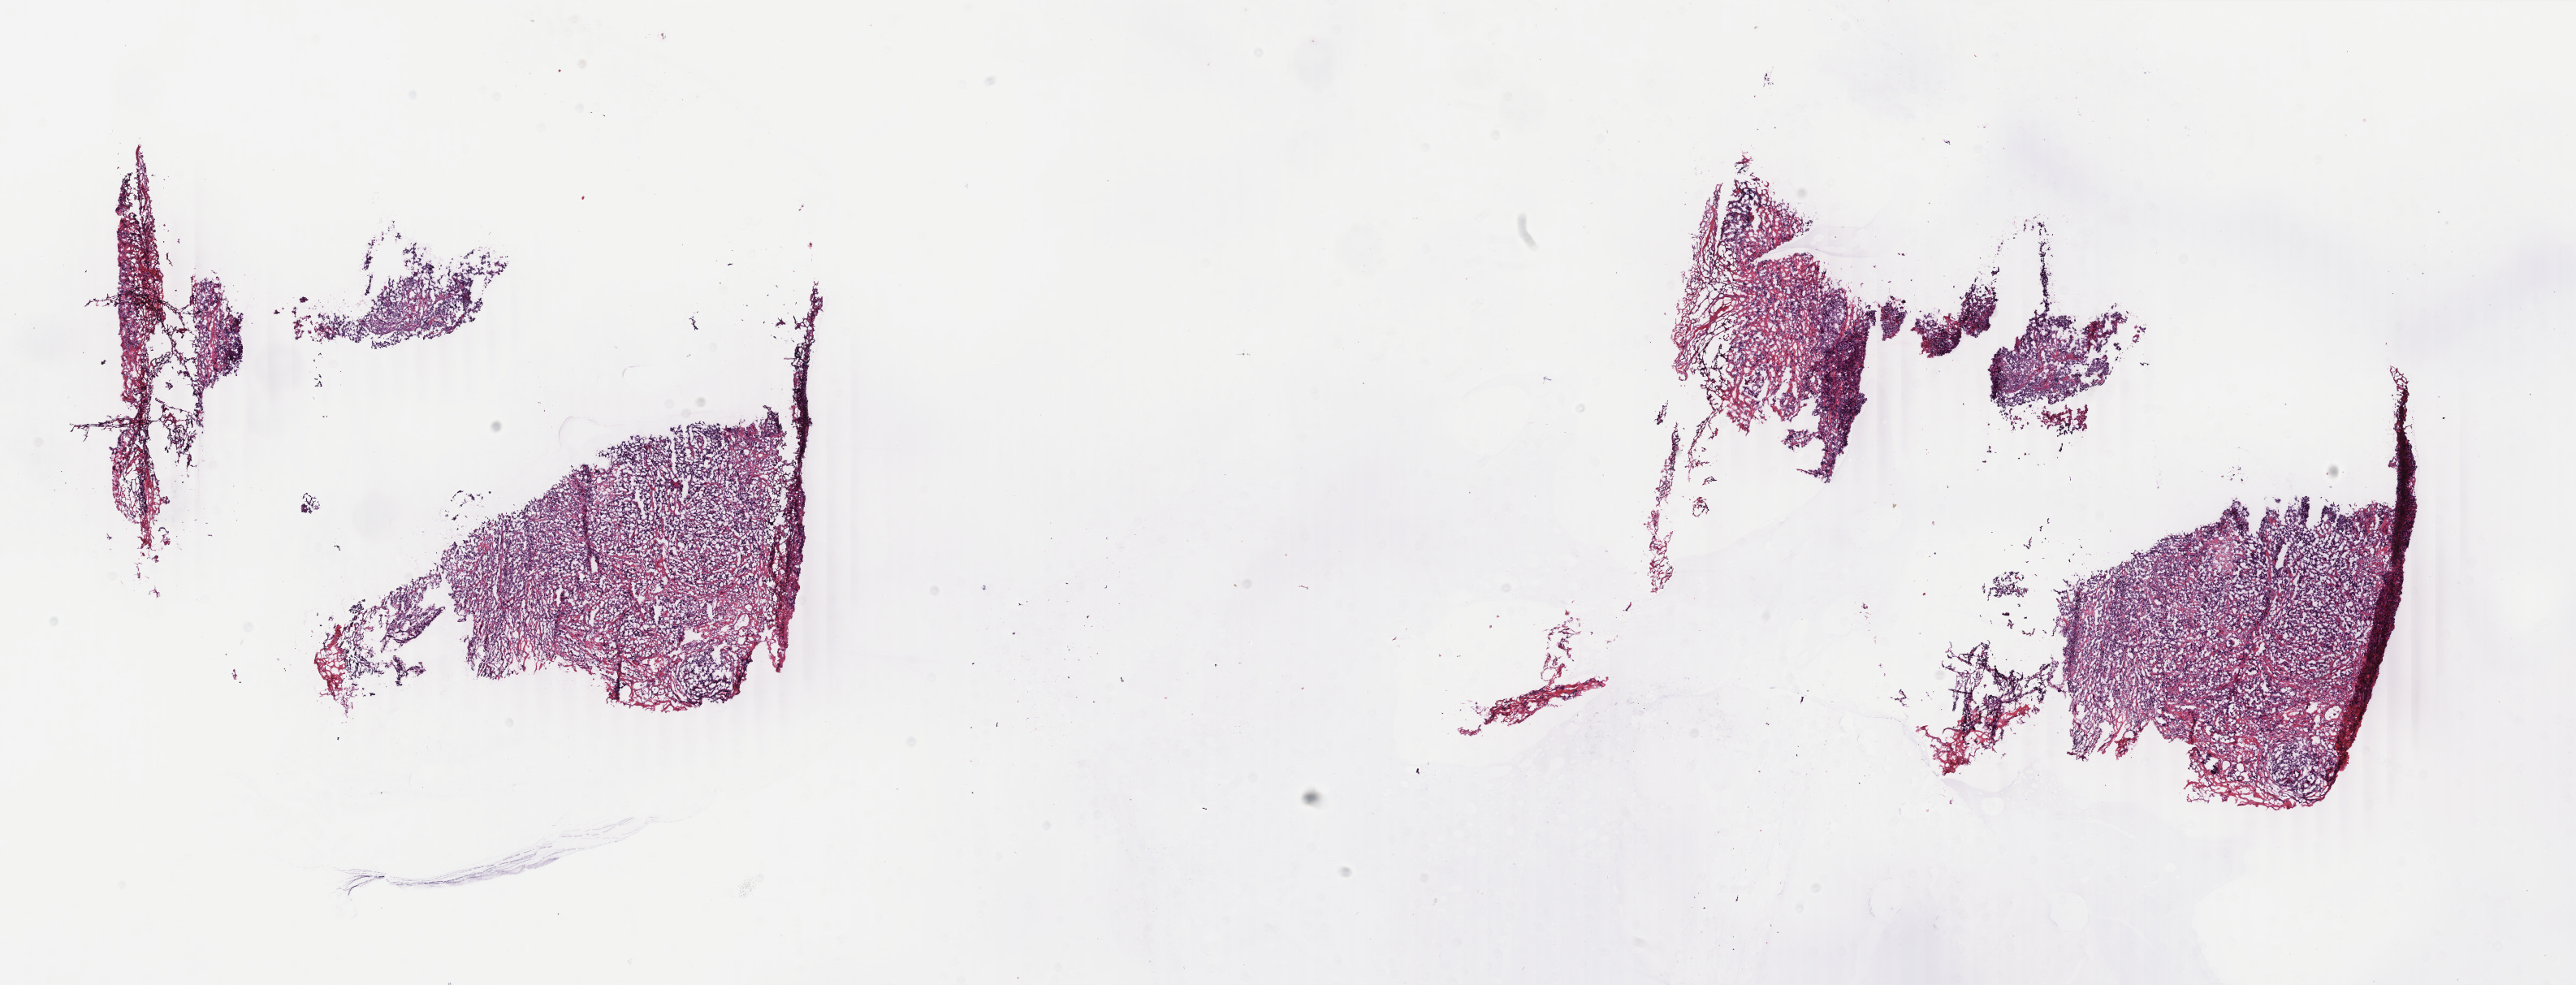
Whole-slide histology image, H&E — low-resolution overview of the scanned area, about 25.2 x 9.6 mm (slide scanned at 40x); frozen section; primary tumour sample from the breast. Female patient; age at initial diagnosis 38 years.
Diagnosis: Infiltrating duct carcinoma, NOS.